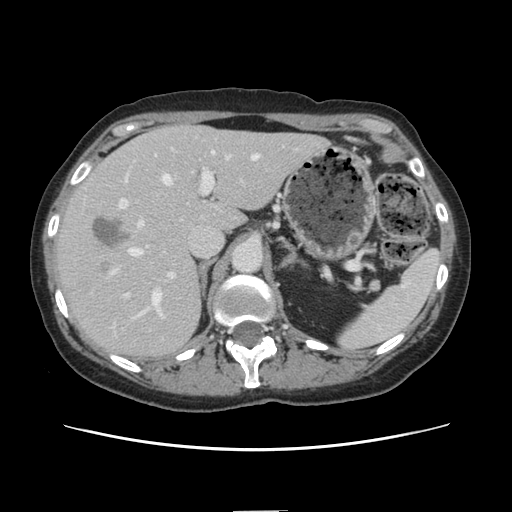
Contrast-enhanced abdominal CT, one axial slice. Position 92 of 141 along the scan axis. Soft-tissue window (W 400 / L 40 HU). 512 × 512 image matrix, field of view 350 × 350 mm. Female patient, age 63 years. Case-level facts recorded for this patient, not image findings: diagnosis: colorectal cancer liver metastases, imaged before liver resection; multiple liver metastases: yes; largest metastasis: 3.2 cm; disease in both lobes: yes.
Annotated regions visible in this slice (expert manual segmentation):
- hepatic veins: box from (x=112, y=152) to (x=258, y=317) px
- liver: (x=56, y=126)–(x=327, y=358)
- planned liver remnant (the part of the liver to remain after resection): (x=181, y=126)–(x=327, y=232)
- portal vein (with intrahepatic branches): (x=118, y=149)–(x=234, y=296)